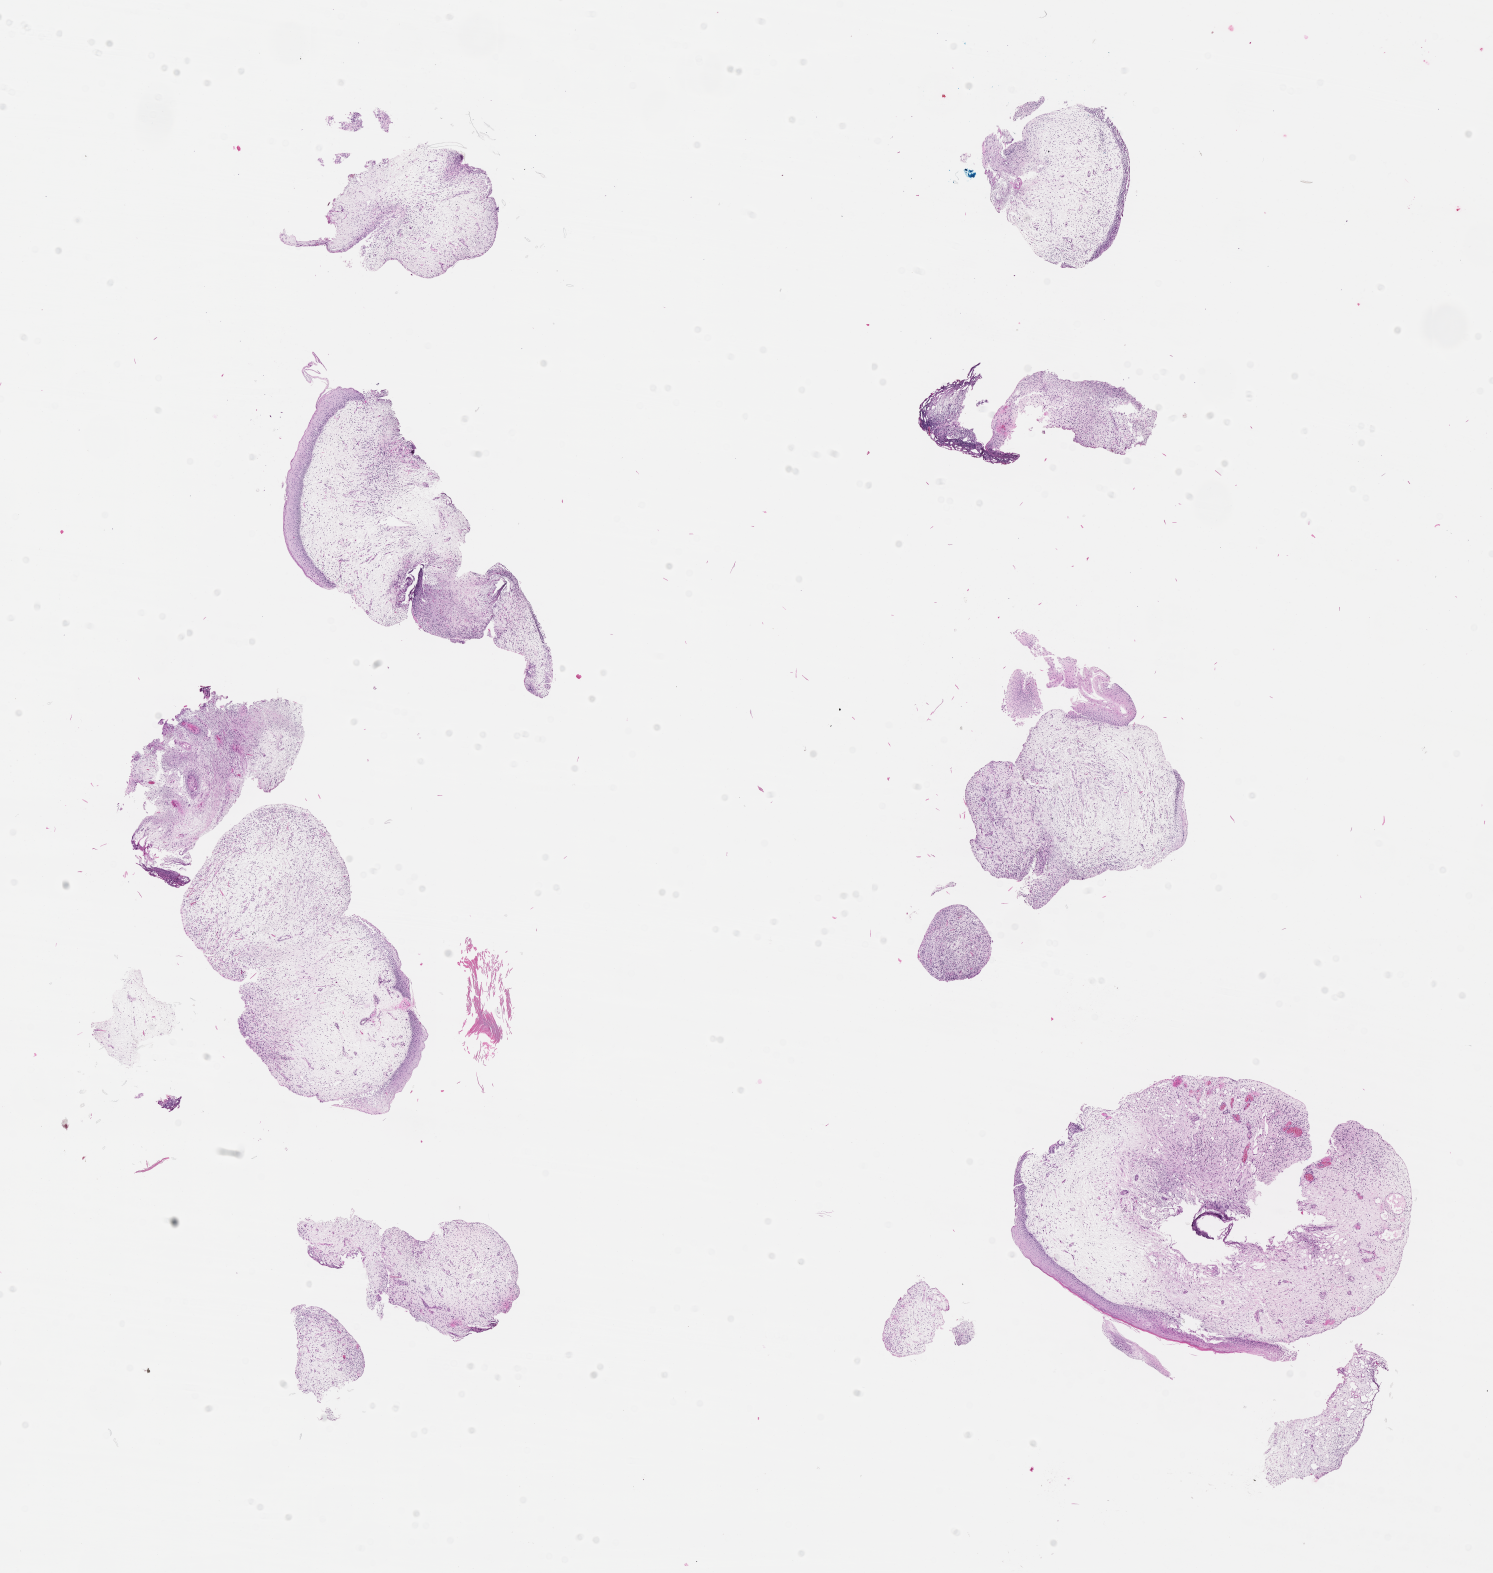
Whole-slide image, haematoxylin and eosin stain of tumor tissue — whole scanned area (about 12.1 x 12.7 mm) shown as a low-resolution overview, formalin-fixed, paraffin-embedded (FFPE) tissue, site: bladder. Male patient, age at diagnosis 1.1 years.
• metastatic status at presentation (as recorded): non-metastatic
• stage (as recorded): 2
• diagnosis: rhabdomyosarcoma; histological classification: embryonal rhabdomyosarcoma